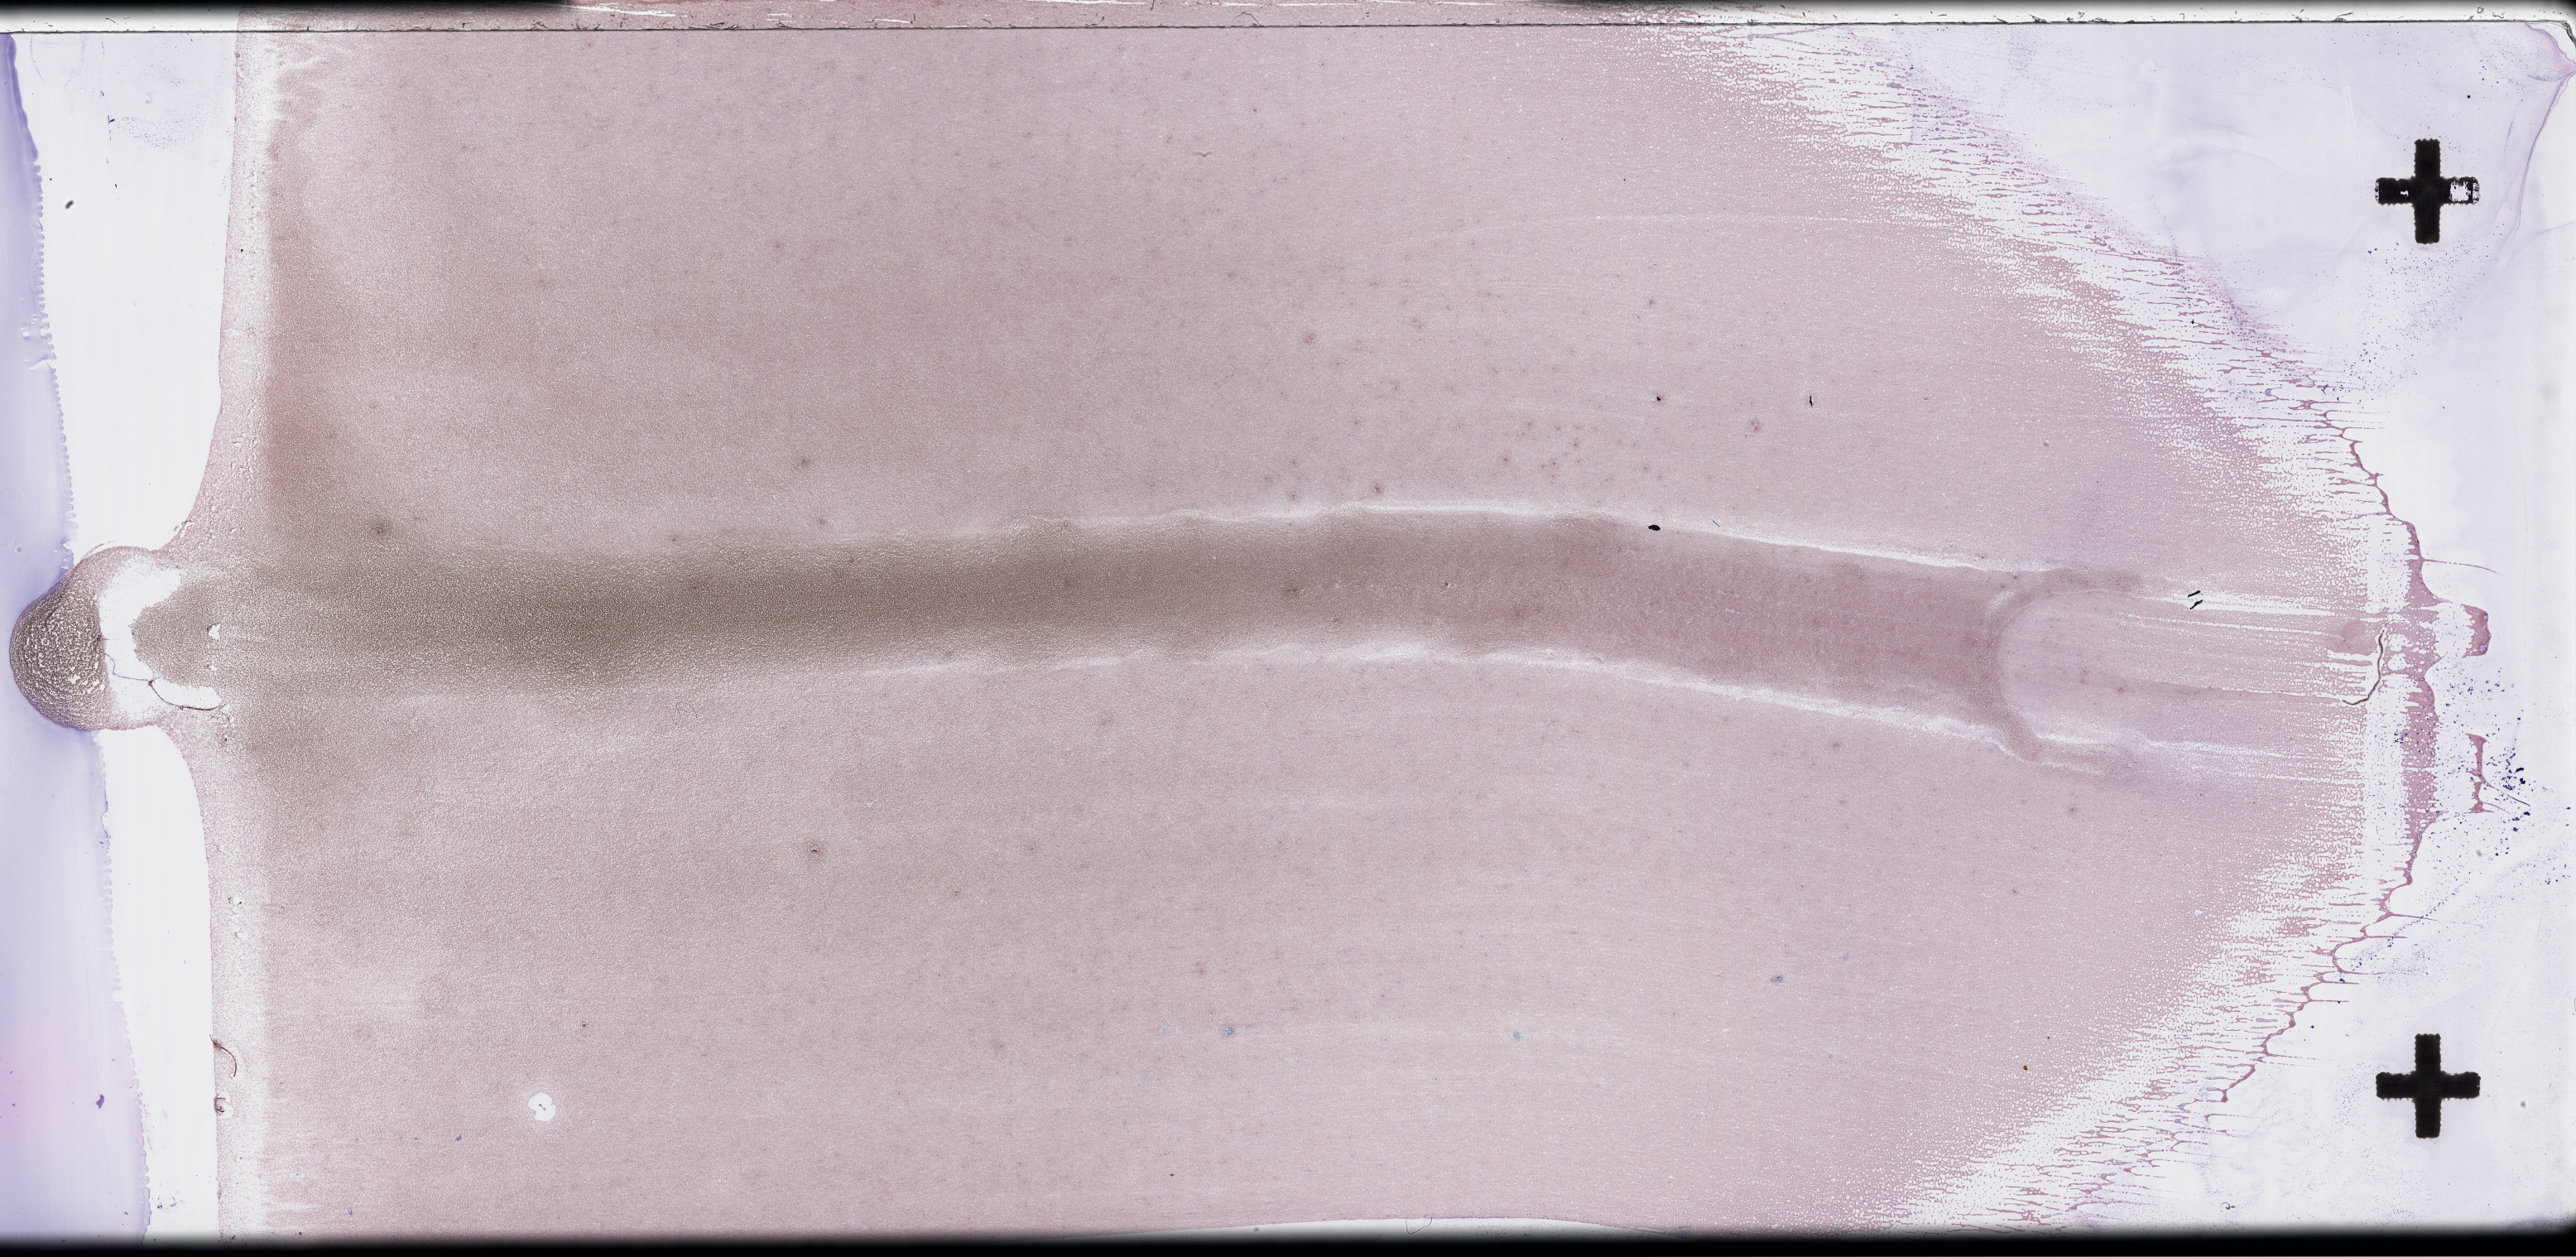
Whole-slide image of a whole blood smear, Wright-Giemsa stain — low-resolution overview of the scanned area, about 50.3 x 24.5 mm. Male patient.
- patient diagnosis: Plasma Cell Myeloma